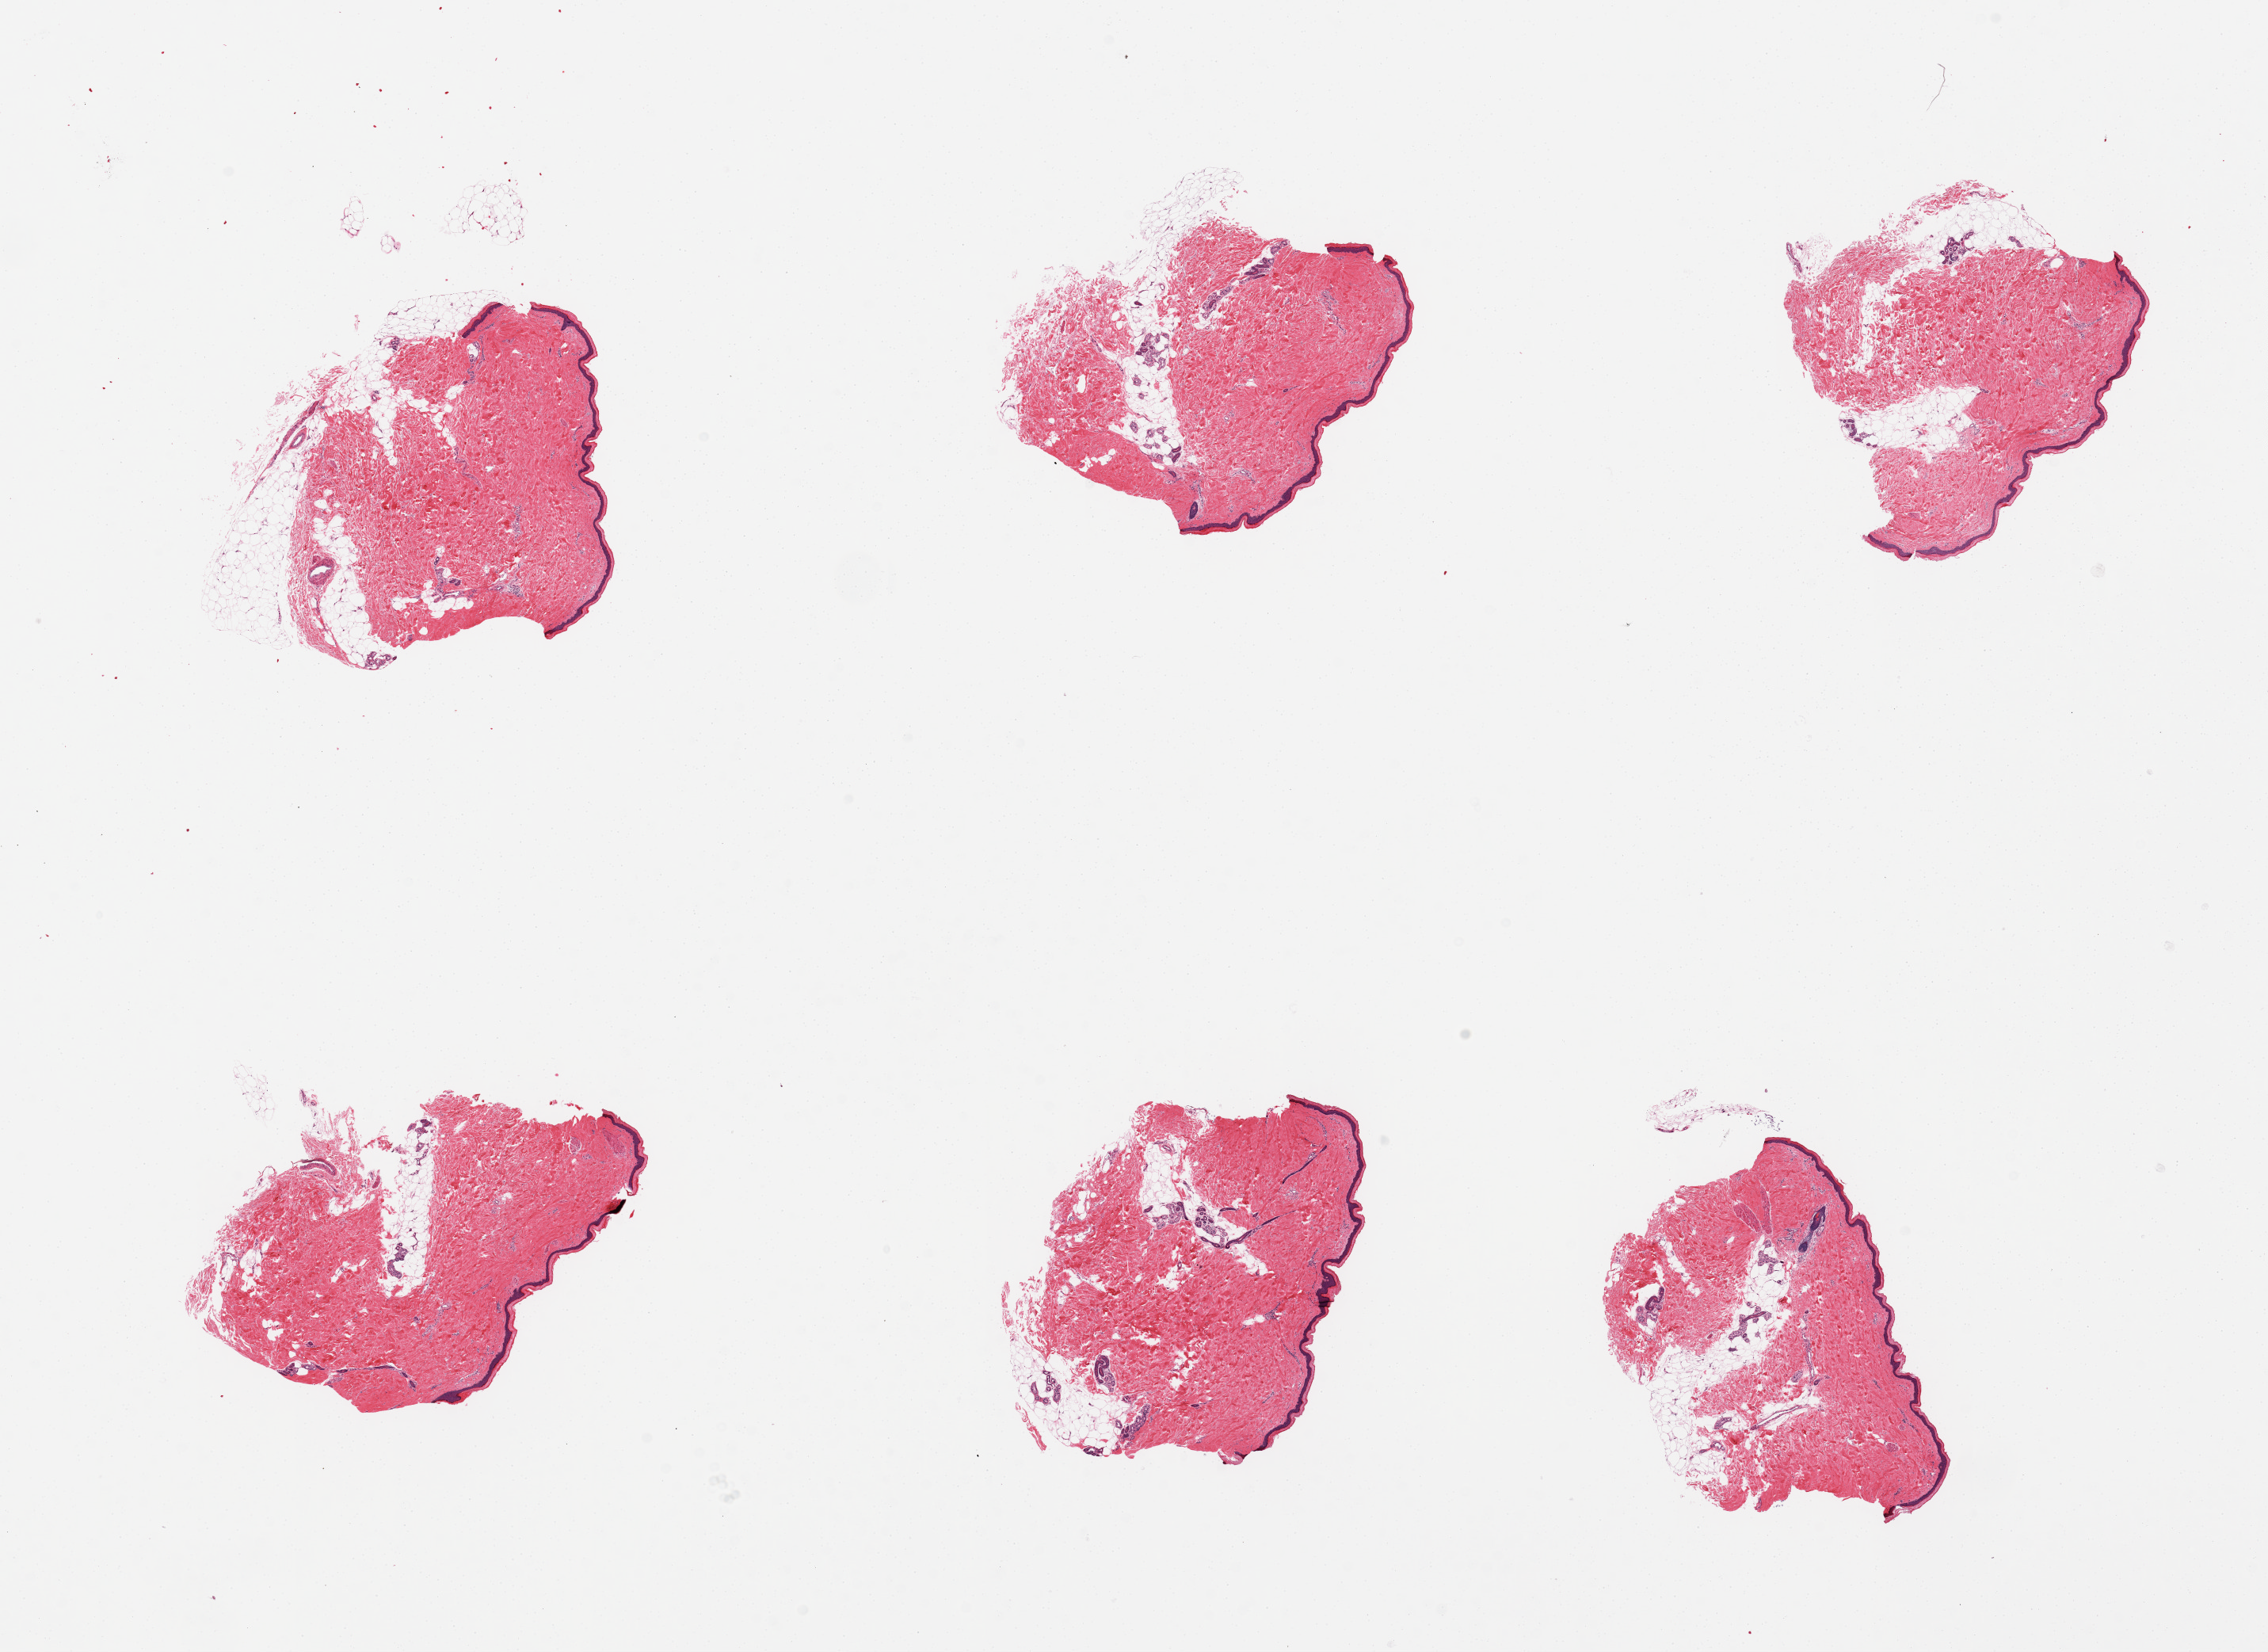
Whole-slide image, hematoxylin and eosin (H&E) stain, brightfield, shown as a low-resolution overview of the whole scanned area (about 22.6 x 16.5 mm, from a 20x scan). PAXgene-fixed, paraffin-embedded tissue. Target tissue: skin of lower leg. Tissue donor sample. Female donor.
* review note (as recorded): 6 pieces, epidermis and dermis with 10-20% attached and internal fat, squamous epithelium measures 35-40 microns